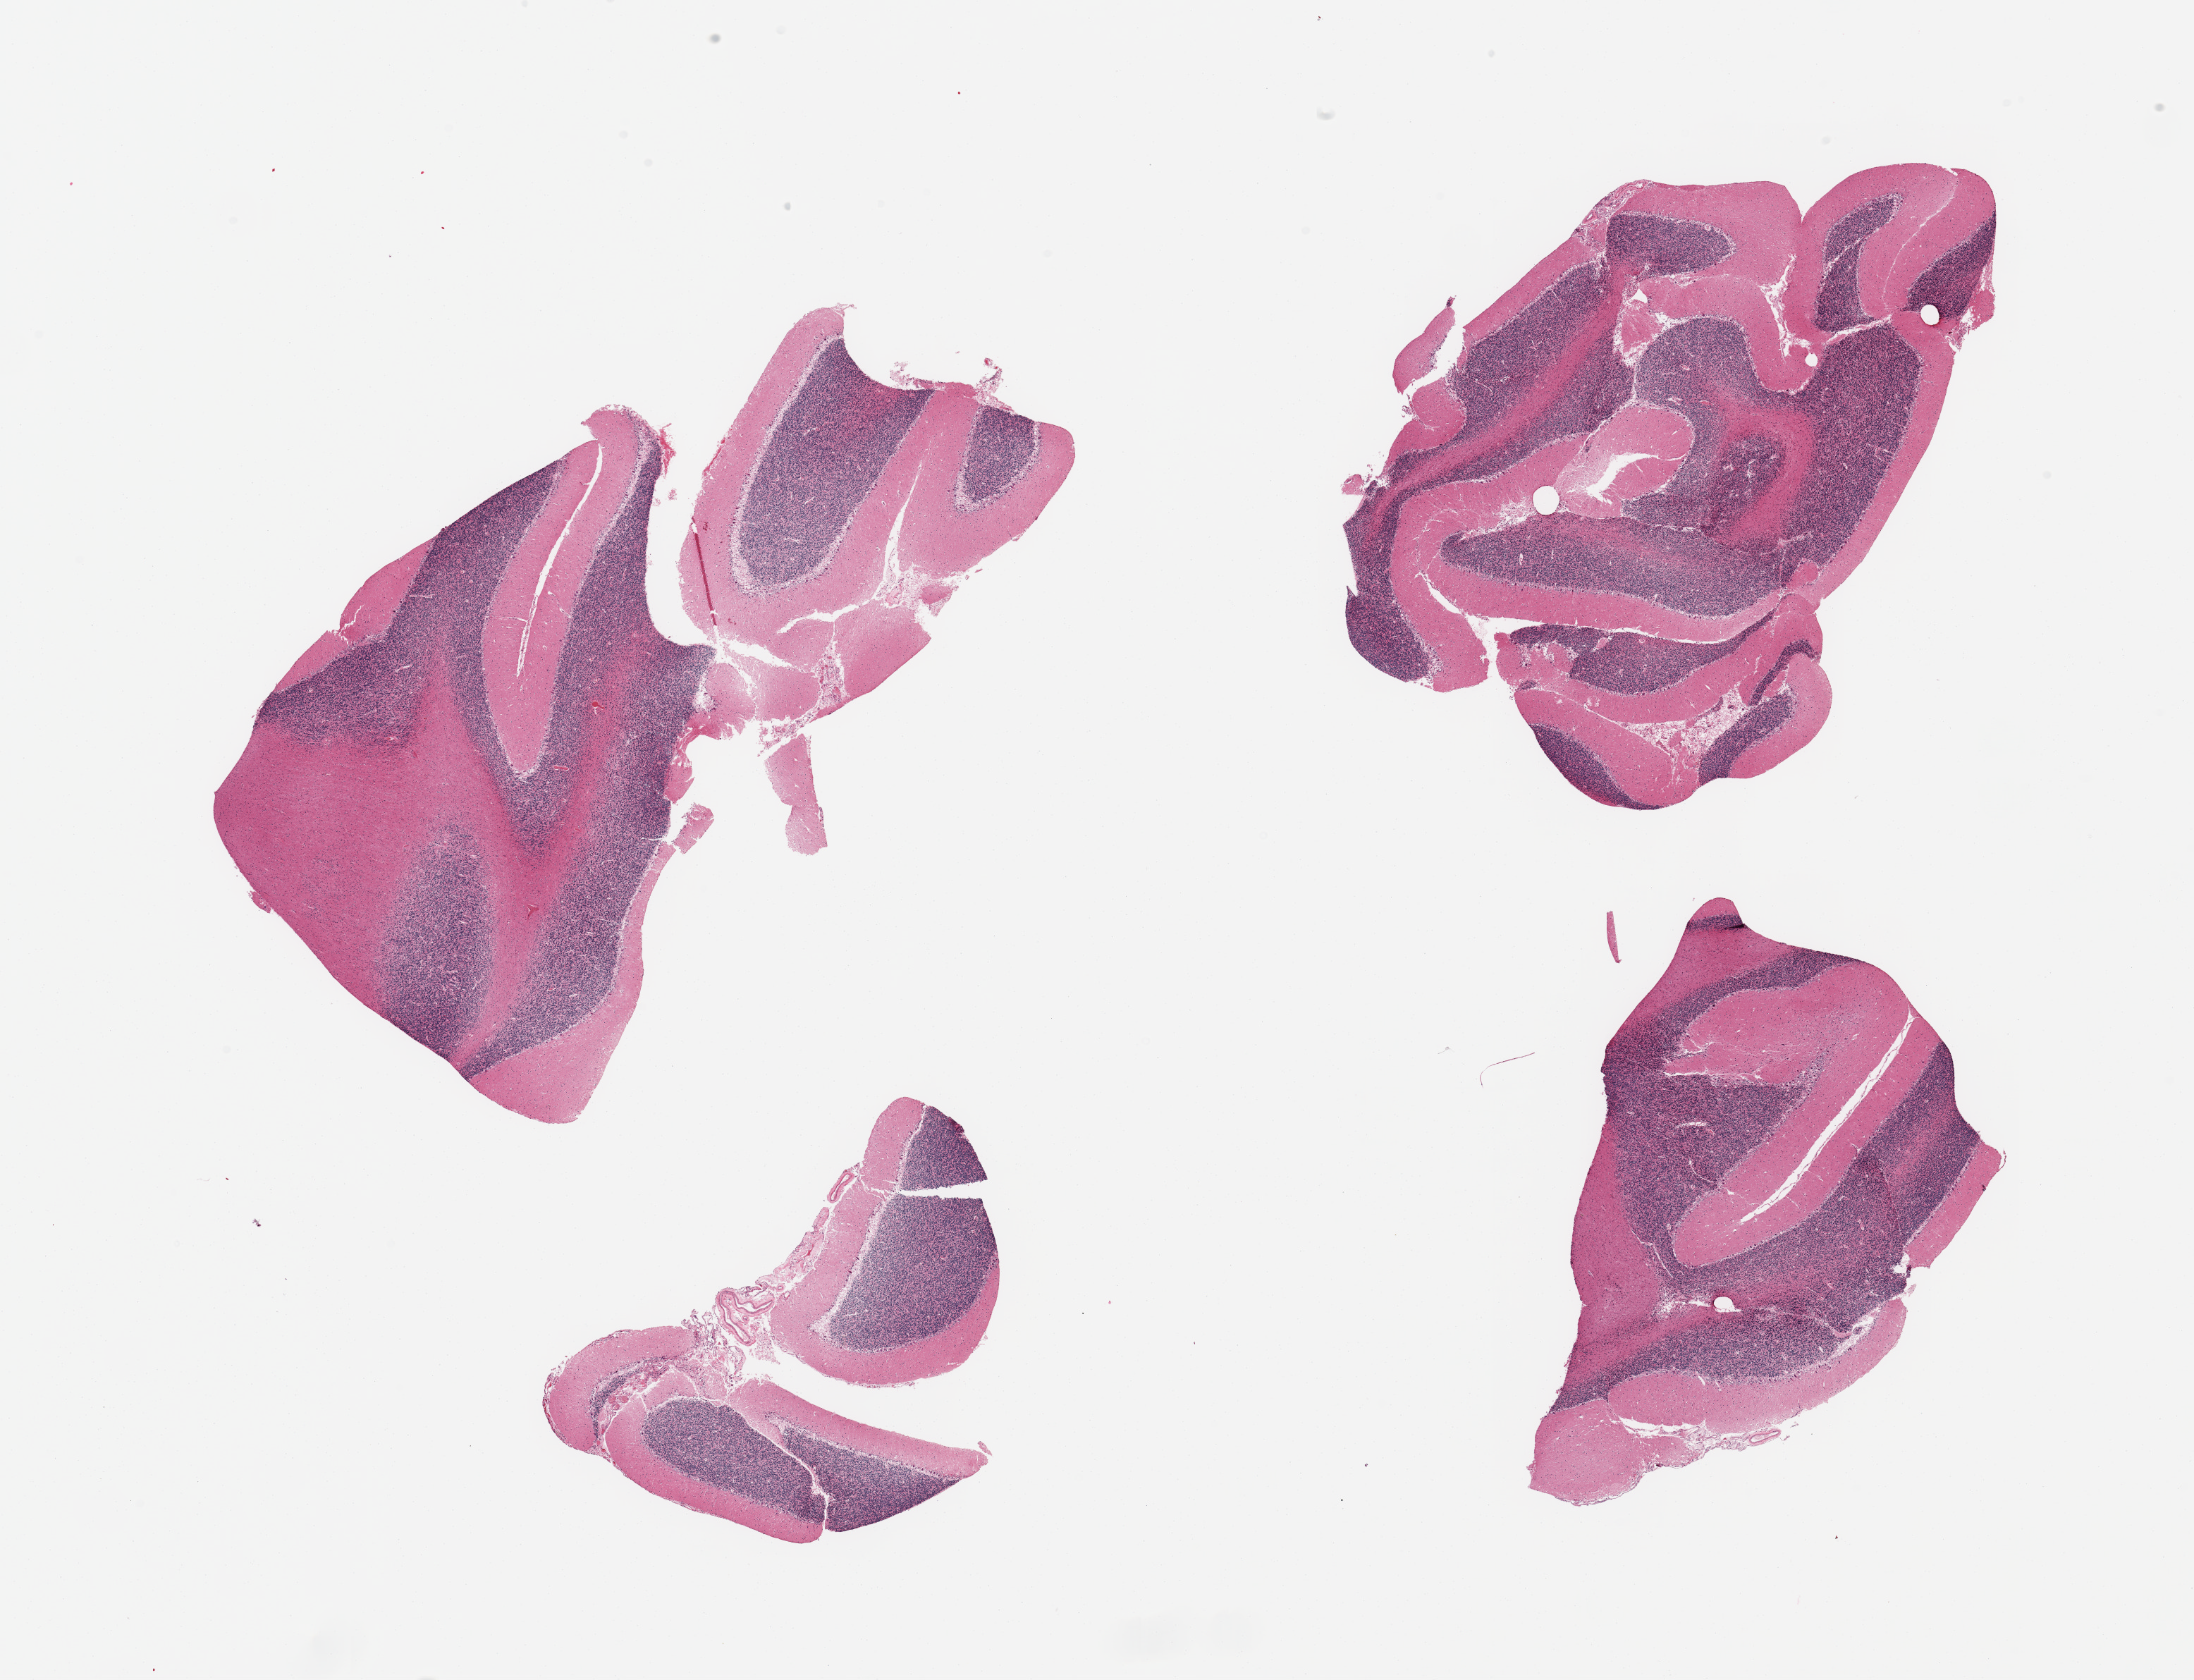
Whole-slide image, haematoxylin and eosin stain, brightfield, whole scanned area (about 24.6 x 18.8 mm) shown as a low-resolution overview; PAXgene-fixed, paraffin-embedded tissue; target tissue: cerebellum; tissue donor sample.
Reviewer comment on this tissue sample: 4 pieces, no abnormalities.